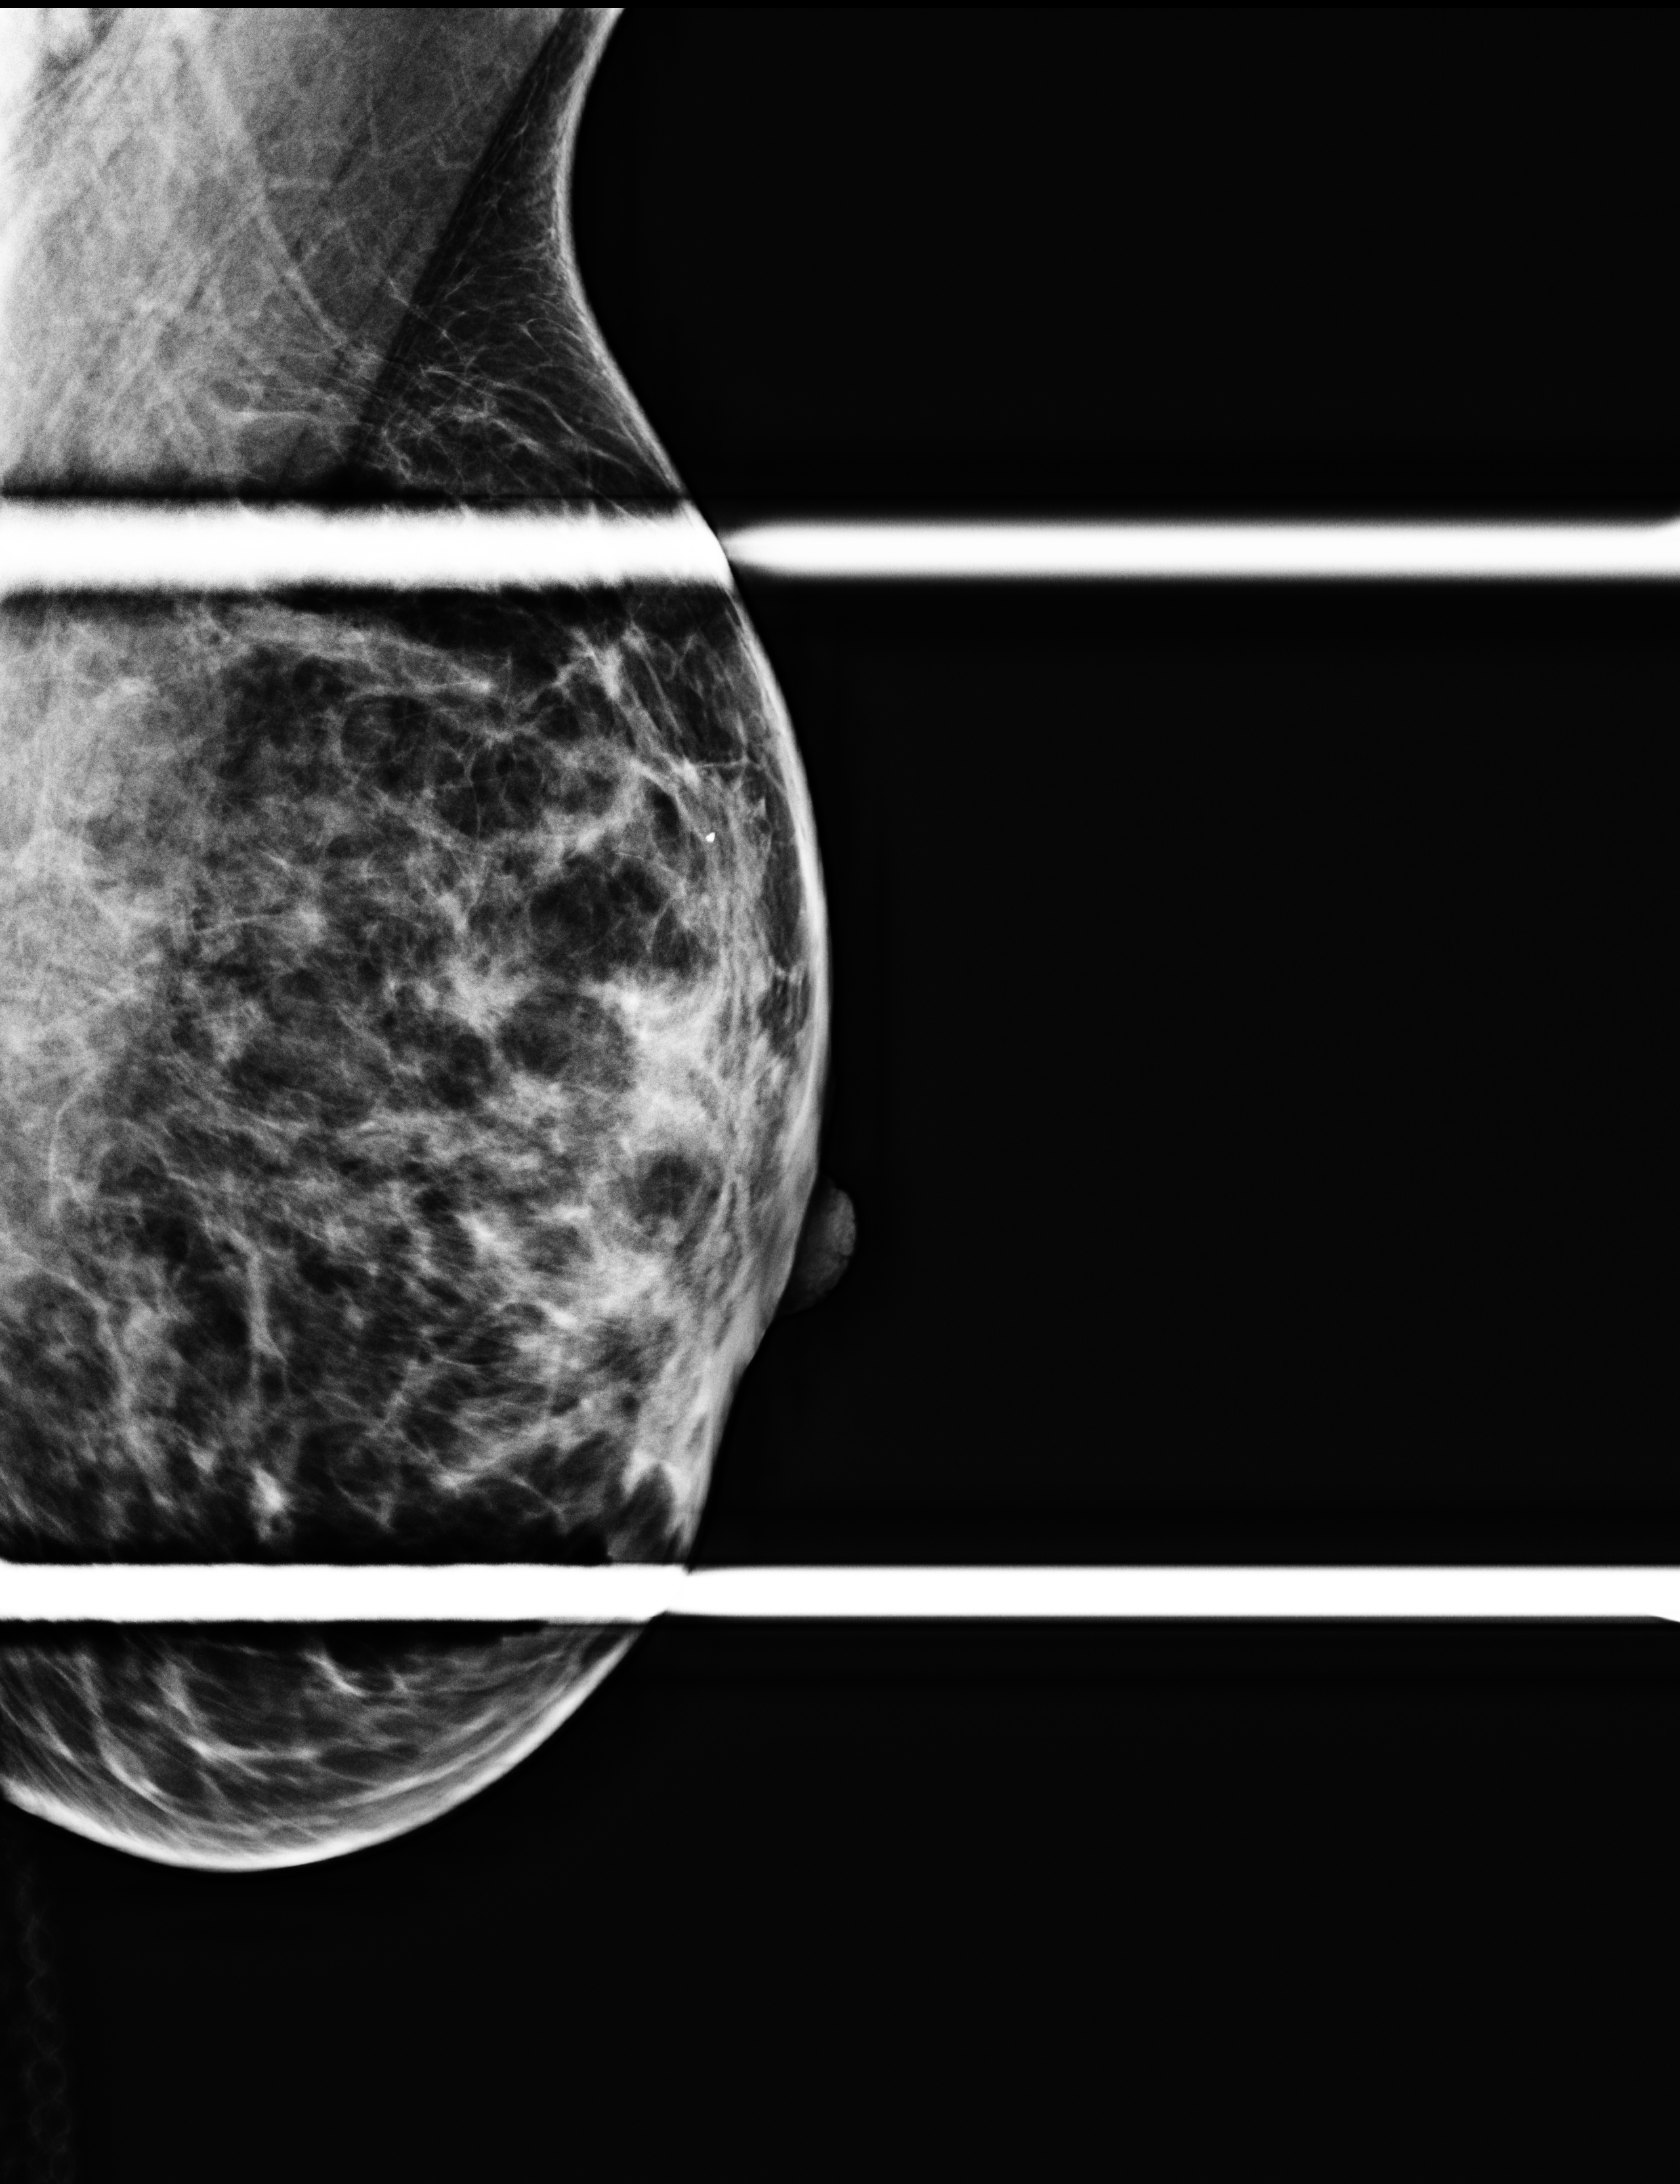
Digital mammogram (FFDM), left breast, medio-lateral oblique projection (spot compression), screening examination, compressed breast thickness 42 mm, system: Selenia Dimensions. Patient aged 43 years (female).
- breast density at the screening exam (both breasts): heterogeneously dense (BI-RADS density category c)
- final BI-RADS category for the screening round (tomosynthesis exam, both breasts): category 2
- recall: no recall after this screen